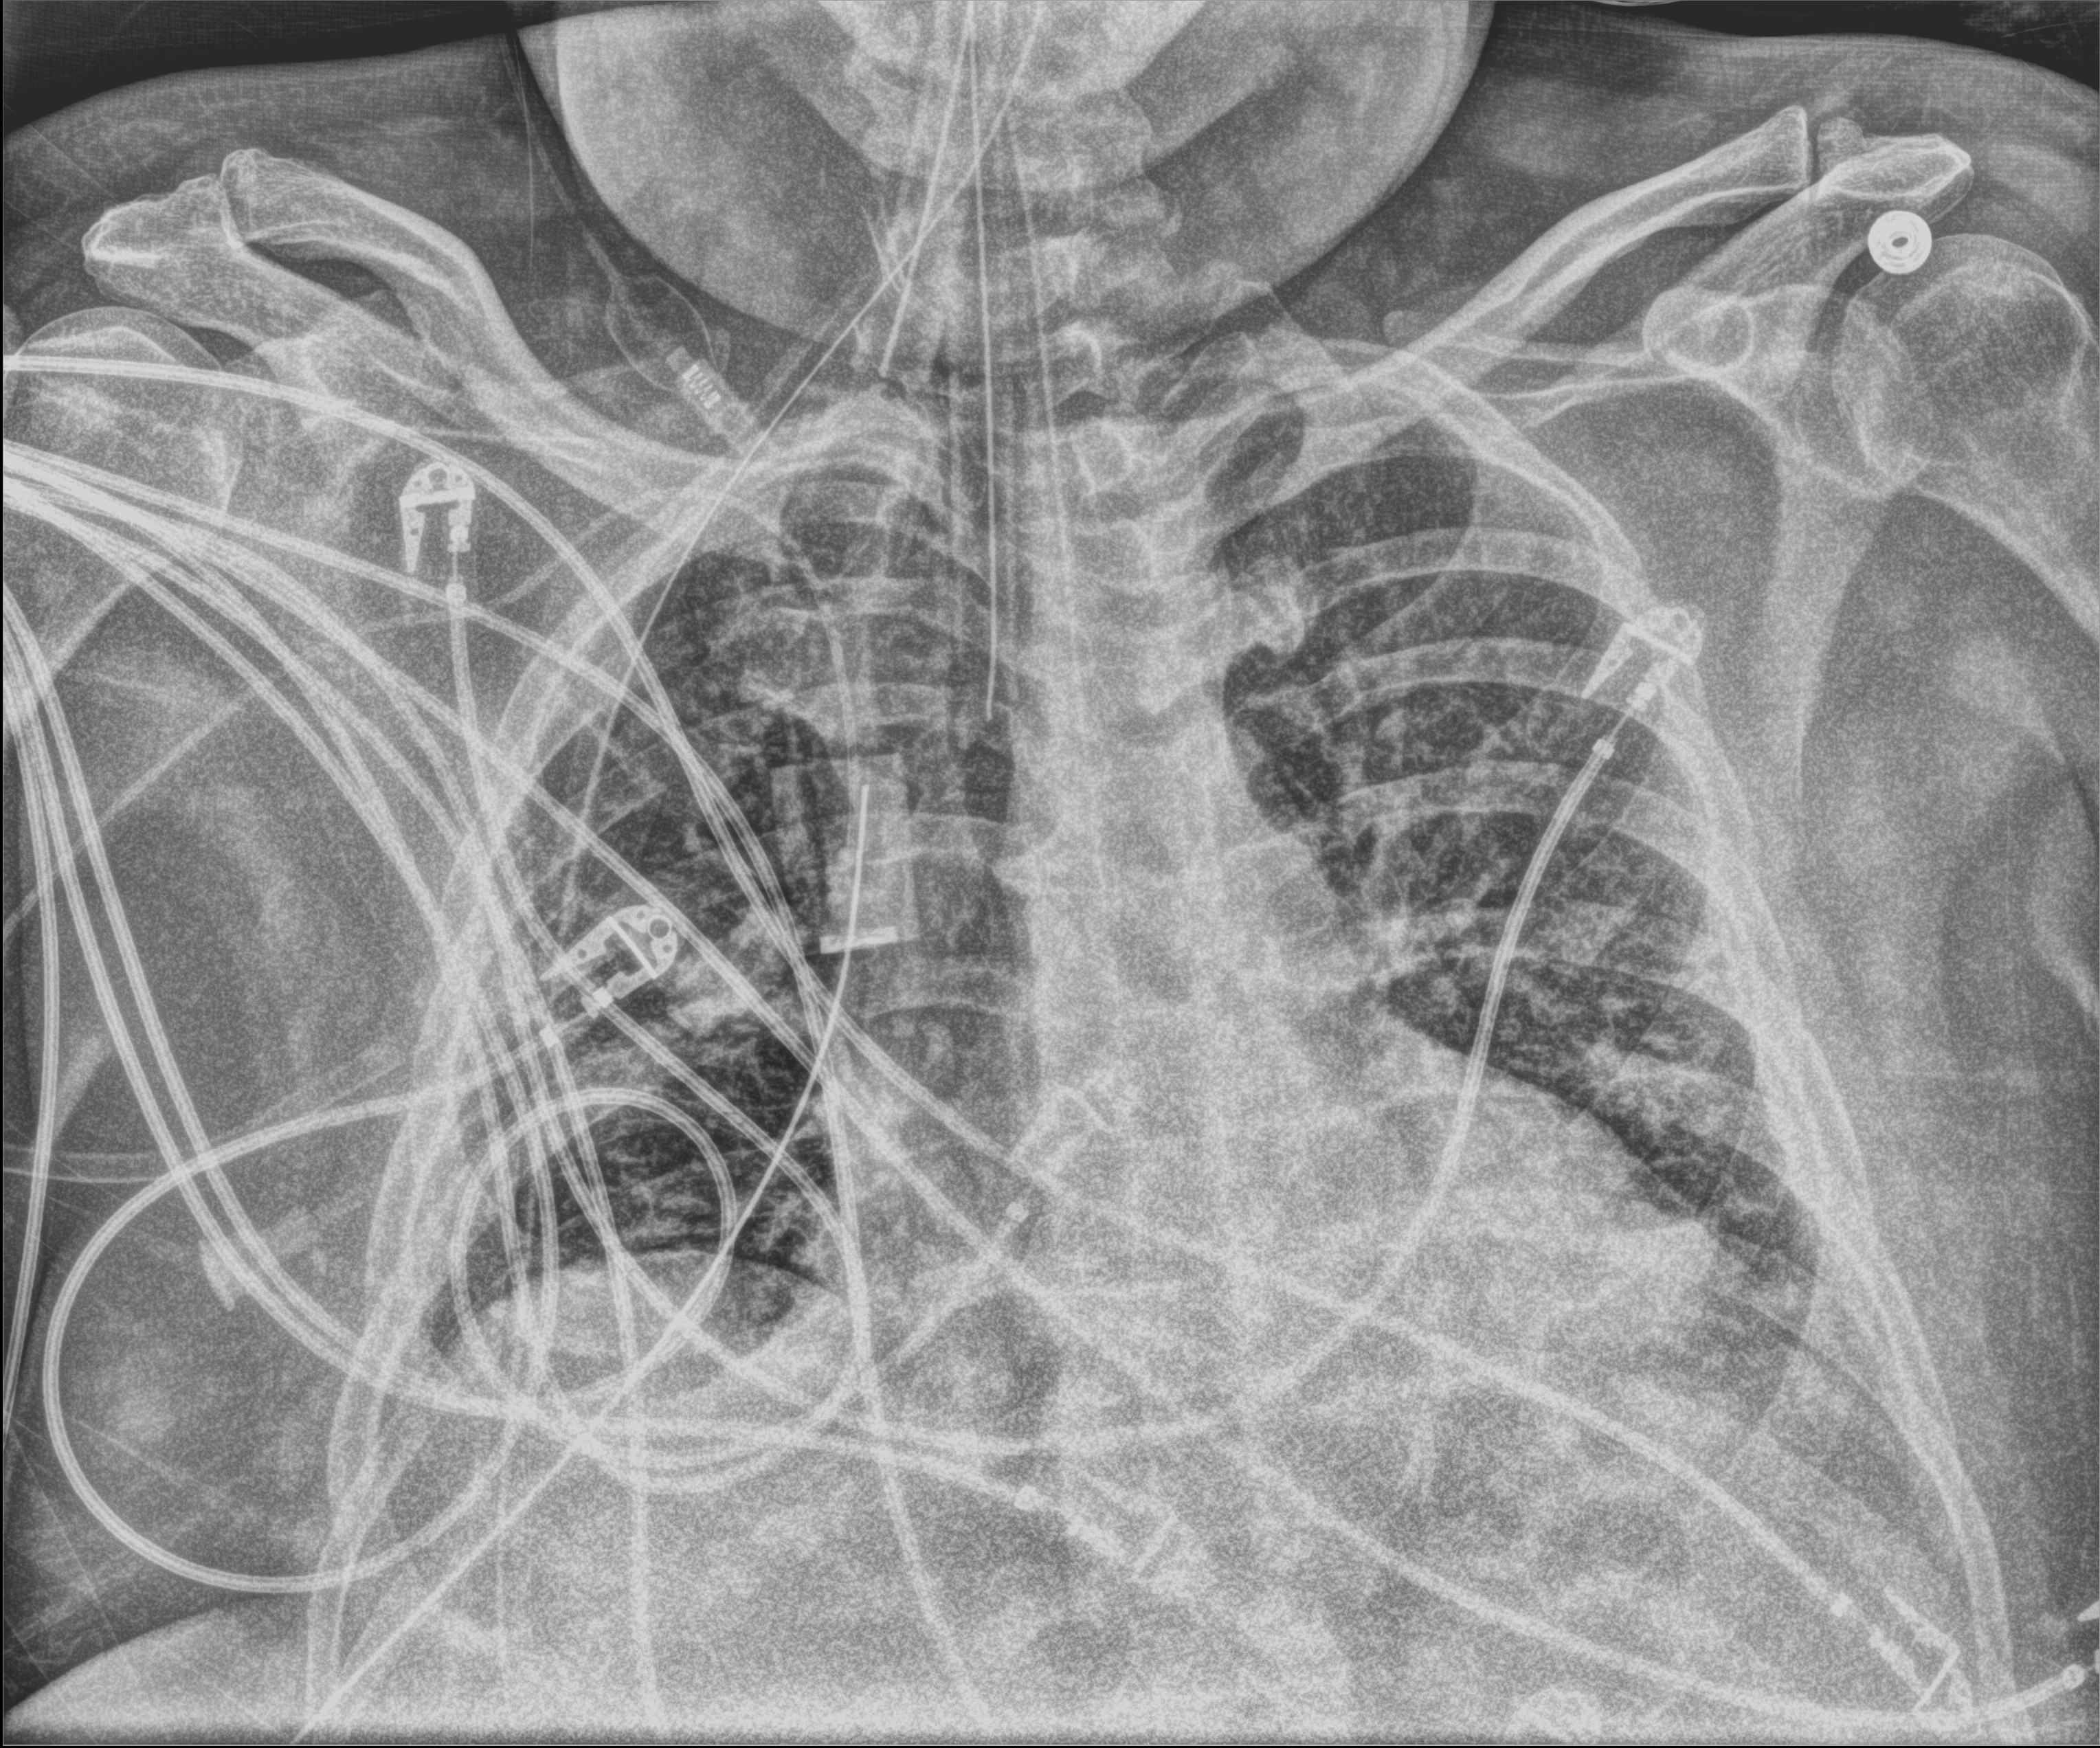
Portable chest radiograph; anteroposterior (AP) projection. Patient hospitalised with COVID-19; male, aged 18–59 years.
Admission-level facts for this patient (not findings on this image; timing relative to this image not recorded): other chronic lung disease (admission record): no.